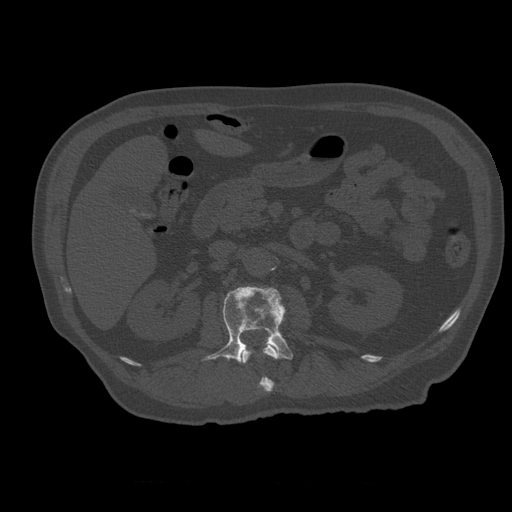
CT including the spine, one axial slice; slice 220 of 399 in the series (ordered by position); reconstruction kernel STANDARD; bone window (W 1800 / L 400 HU); 1.25 mm slice thickness; 512 × 512 image matrix. Patient age 73 years. From the clinical record (not read from this slice): primary cancer: prostate; vertebrae with lytic lesions (as recorded): L2.
Outlined on this slice (semi-automatic segmentation, software-assisted and operator-edited):
- L1 vertebra: bounding box (x1, y1, x2, y2) in pixels: (241, 344, 278, 393)
- L2 vertebra: (202, 286, 294, 363)